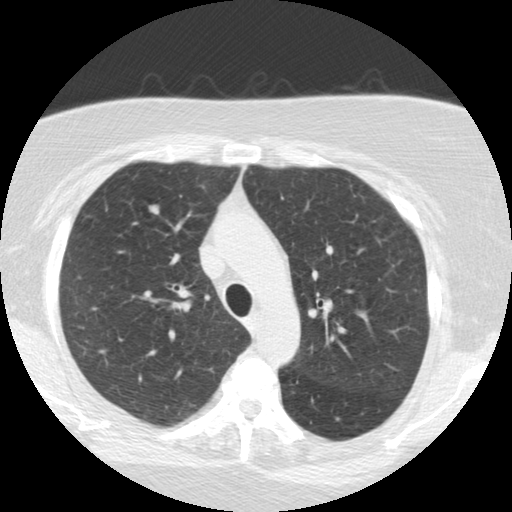
Low-dose screening chest CT, one axial slice. Slice 168 of 225 in the series (ordered by position). Reconstruction kernel STANDARD. Lung window (W 1500 / L -600 HU). 512 × 512 image matrix.
Outlined on this slice (expert manual segmentation):
- lesion 1 (tumor, upper lobe of right lung): box from (x=149, y=205) to (x=159, y=215) px